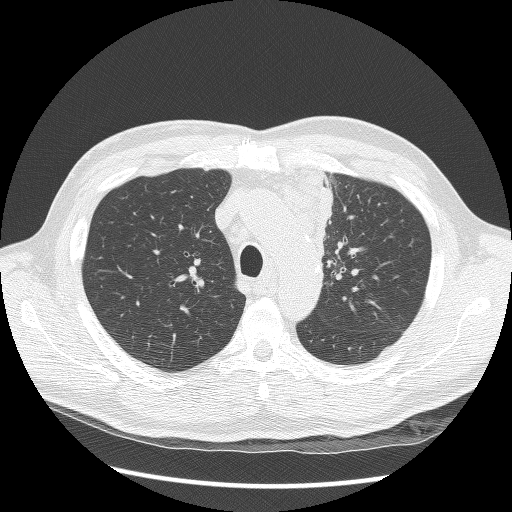
Low-dose screening chest CT, axial slice. Second screening round (one year after baseline). Lung window (W 1500 / L -600 HU). 2.5 mm slice thickness. 120 kVp. 512 × 512 image matrix, field of view 360 × 360 mm. Male, age 64 years at enrolment.
Lesion marked by an expert reader, bounding box [x1, y1, x2, y2] px = [294, 178, 363, 294]. Screening reader's record for this exam: no non-calcified nodule ≥4 mm recorded. Official screen result: positive, other. Lung cancer was diagnosed 24 days after this screen: small cell carcinoma, NOS, left upper lobe, stage IV (AJCC 6th edition), 100 mm at pathology.